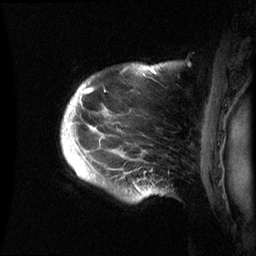
Breast MRI (dynamic contrast-enhanced), one sagittal slice. Dynamic contrast-enhanced series, image 2 of 3 at this slice position (ordered by acquisition). 1.5 T. TE 4.2 ms, TR 8.4 ms. 2.4 mm slice thickness. 256 × 256 image matrix. Patient: female, 48 years.
Structures marked on this image (semi-automatic segmentation, software-assisted and operator-edited):
- analysis volume of interest (the breast-tissue region the enhancement analysis was run in; not a lesion): box from (x=61, y=64) to (x=166, y=201) px
- tumour enhancement mask (voxels above the 70 % enhancement threshold inside the analysis volume of interest): (x=62, y=66)–(x=153, y=191)